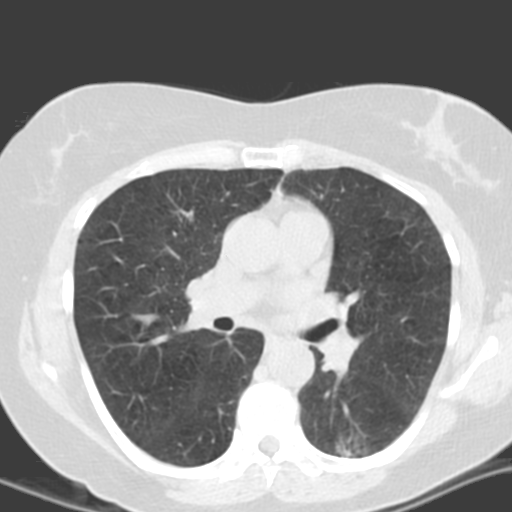
Low-dose screening chest CT, axial slice. Second annual screen. Lung window (W 1500 / L -600 HU). 3.2 mm slice thickness. Standard (soft-tissue) reconstruction kernel (B). Female, age 55 years at enrolment. Current smoker at enrolment.
• Expert reader's lesion annotation, bounding box <304,409,382,473> (left, top, right, bottom; pixels).
• The screening reader recorded 4 non-calcified nodules or masses ≥4 mm on this exam (left lower lobe, left lower lobe, left upper lobe, right middle lobe); which of them this box marks is not recorded.
• Lung cancer was diagnosed 688 days after this screen: adenocarcinoma with mixed subtypes, left lower lobe, poorly differentiated (G3), stage IA (AJCC 6th edition), 21 mm at pathology.